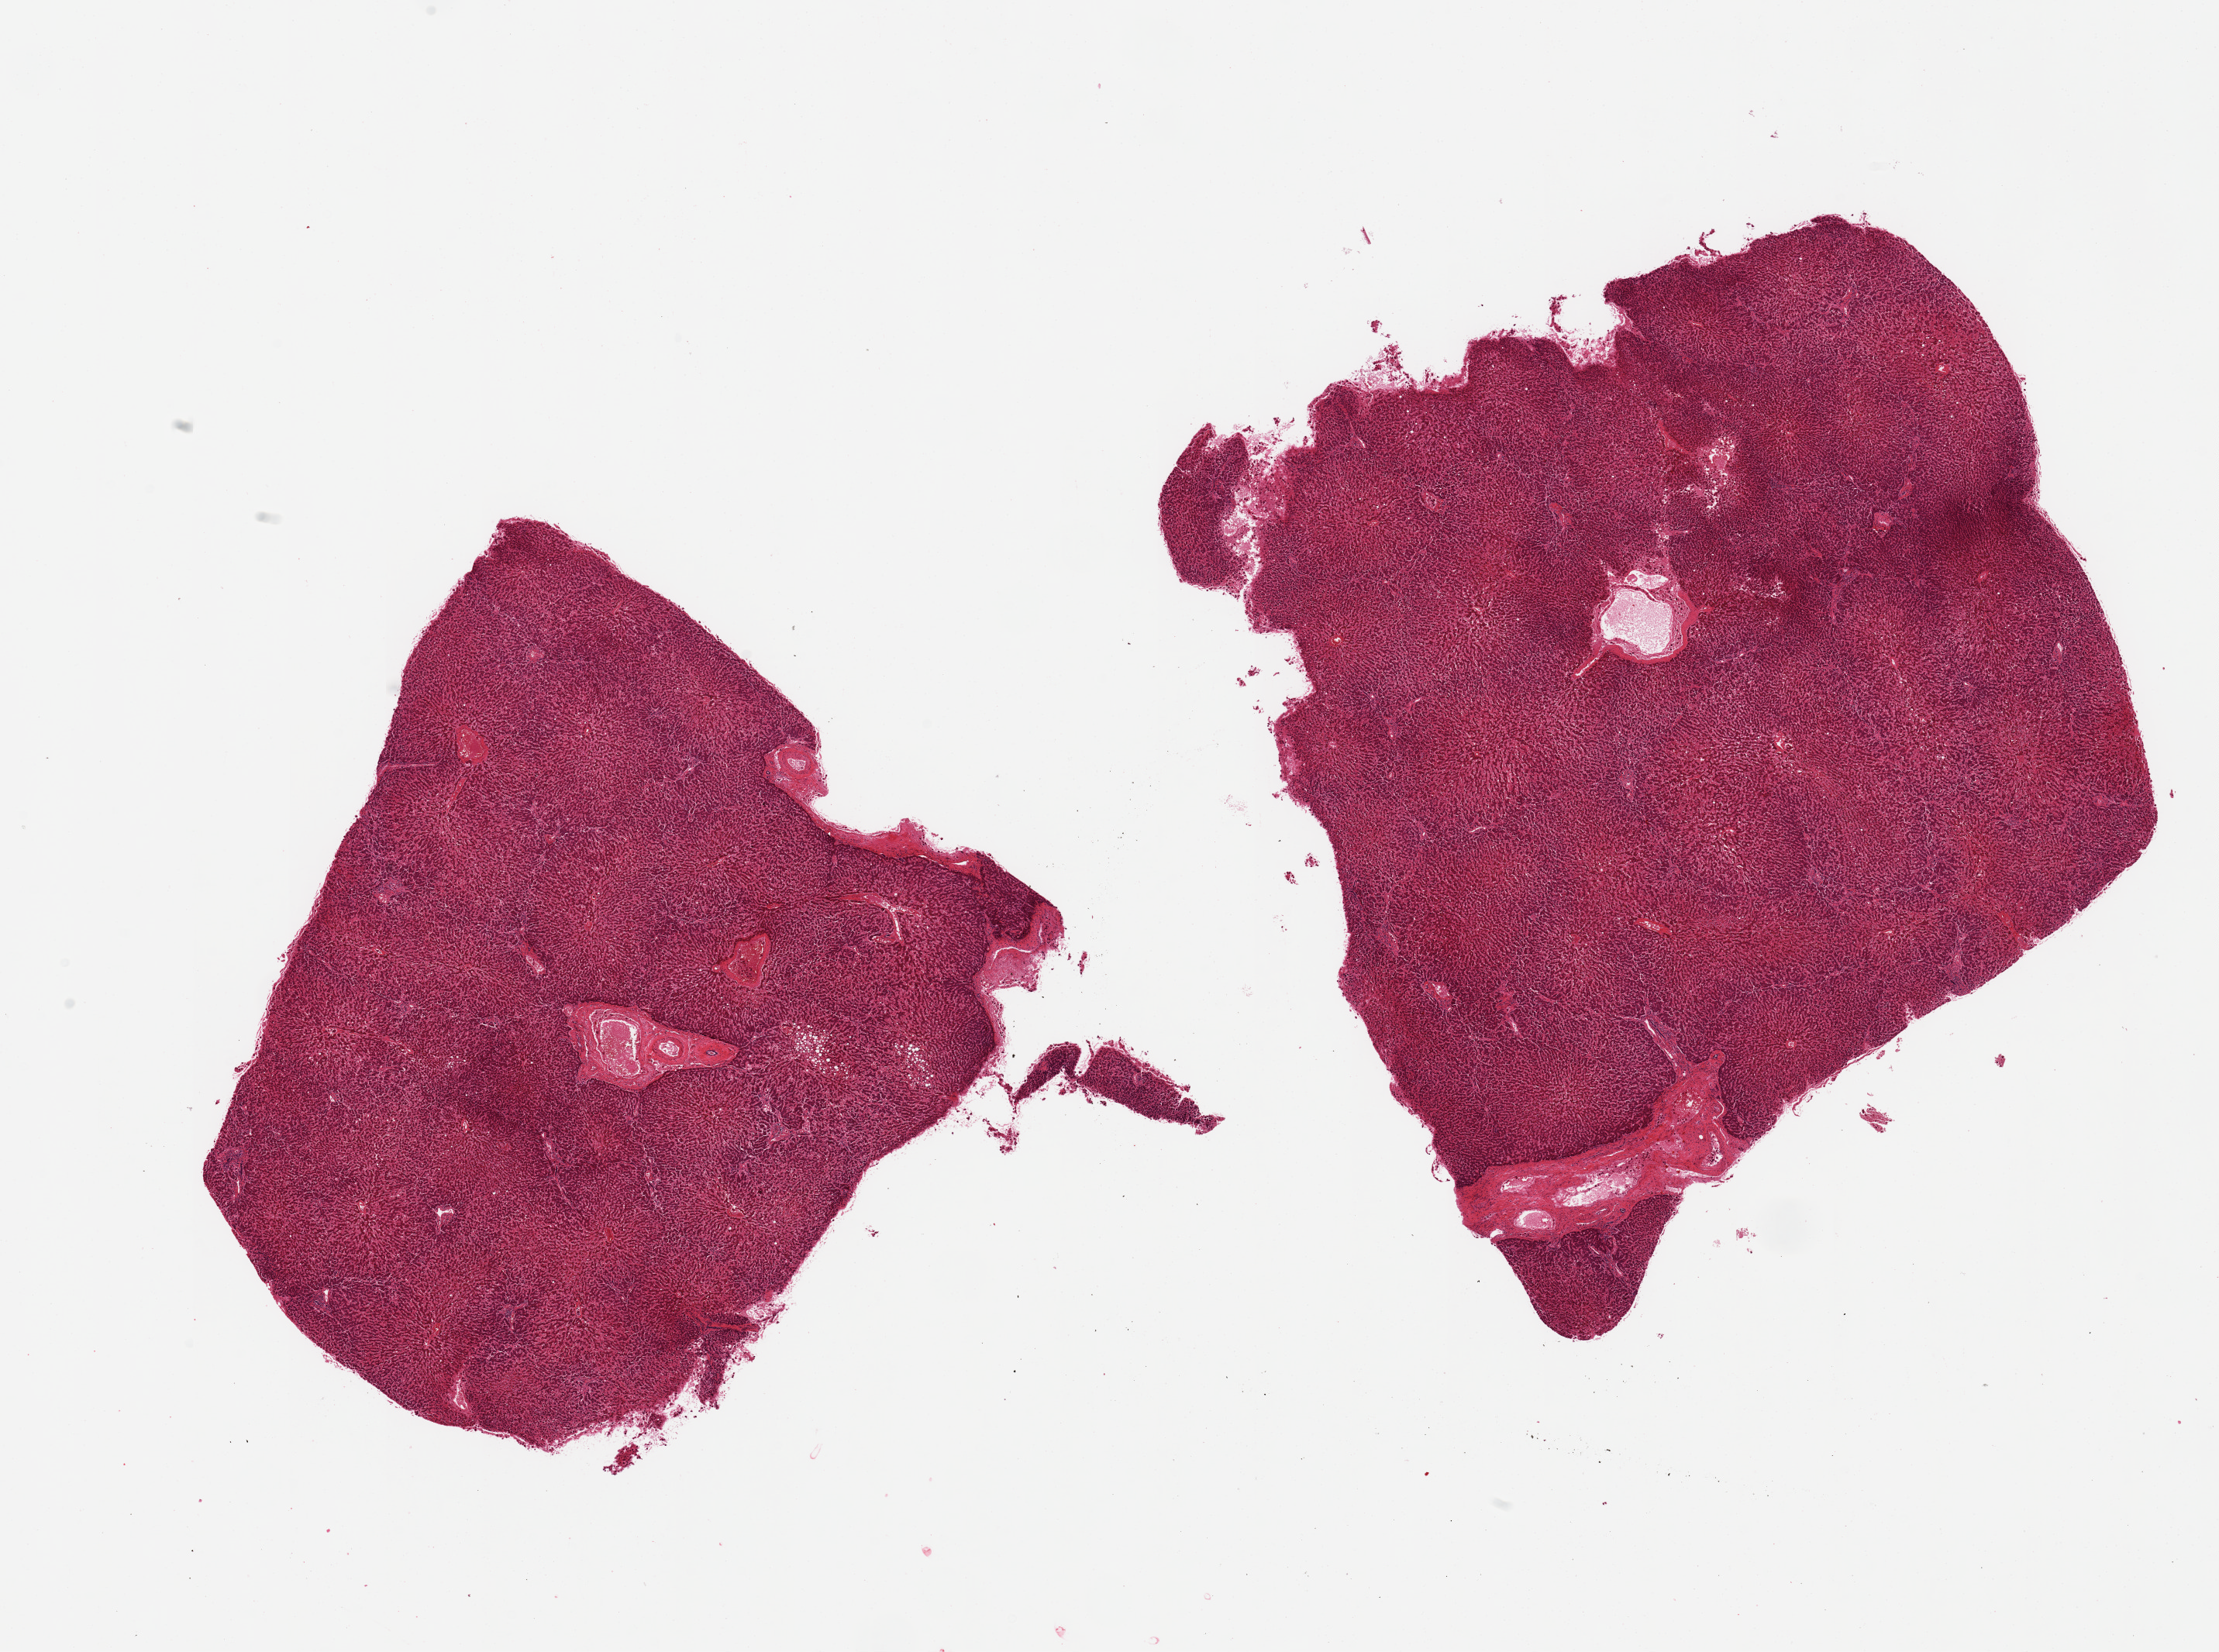
Digitized hematoxylin and eosin (H&E)-stained section — a low-resolution overview of the entire scanned area, about 22.6 x 16.9 mm, PAXgene-fixed paraffin-embedded (PFPE) section, target tissue: liver, tissue donor sample. Donor sex: female.
• review note (as recorded): 2 pieces